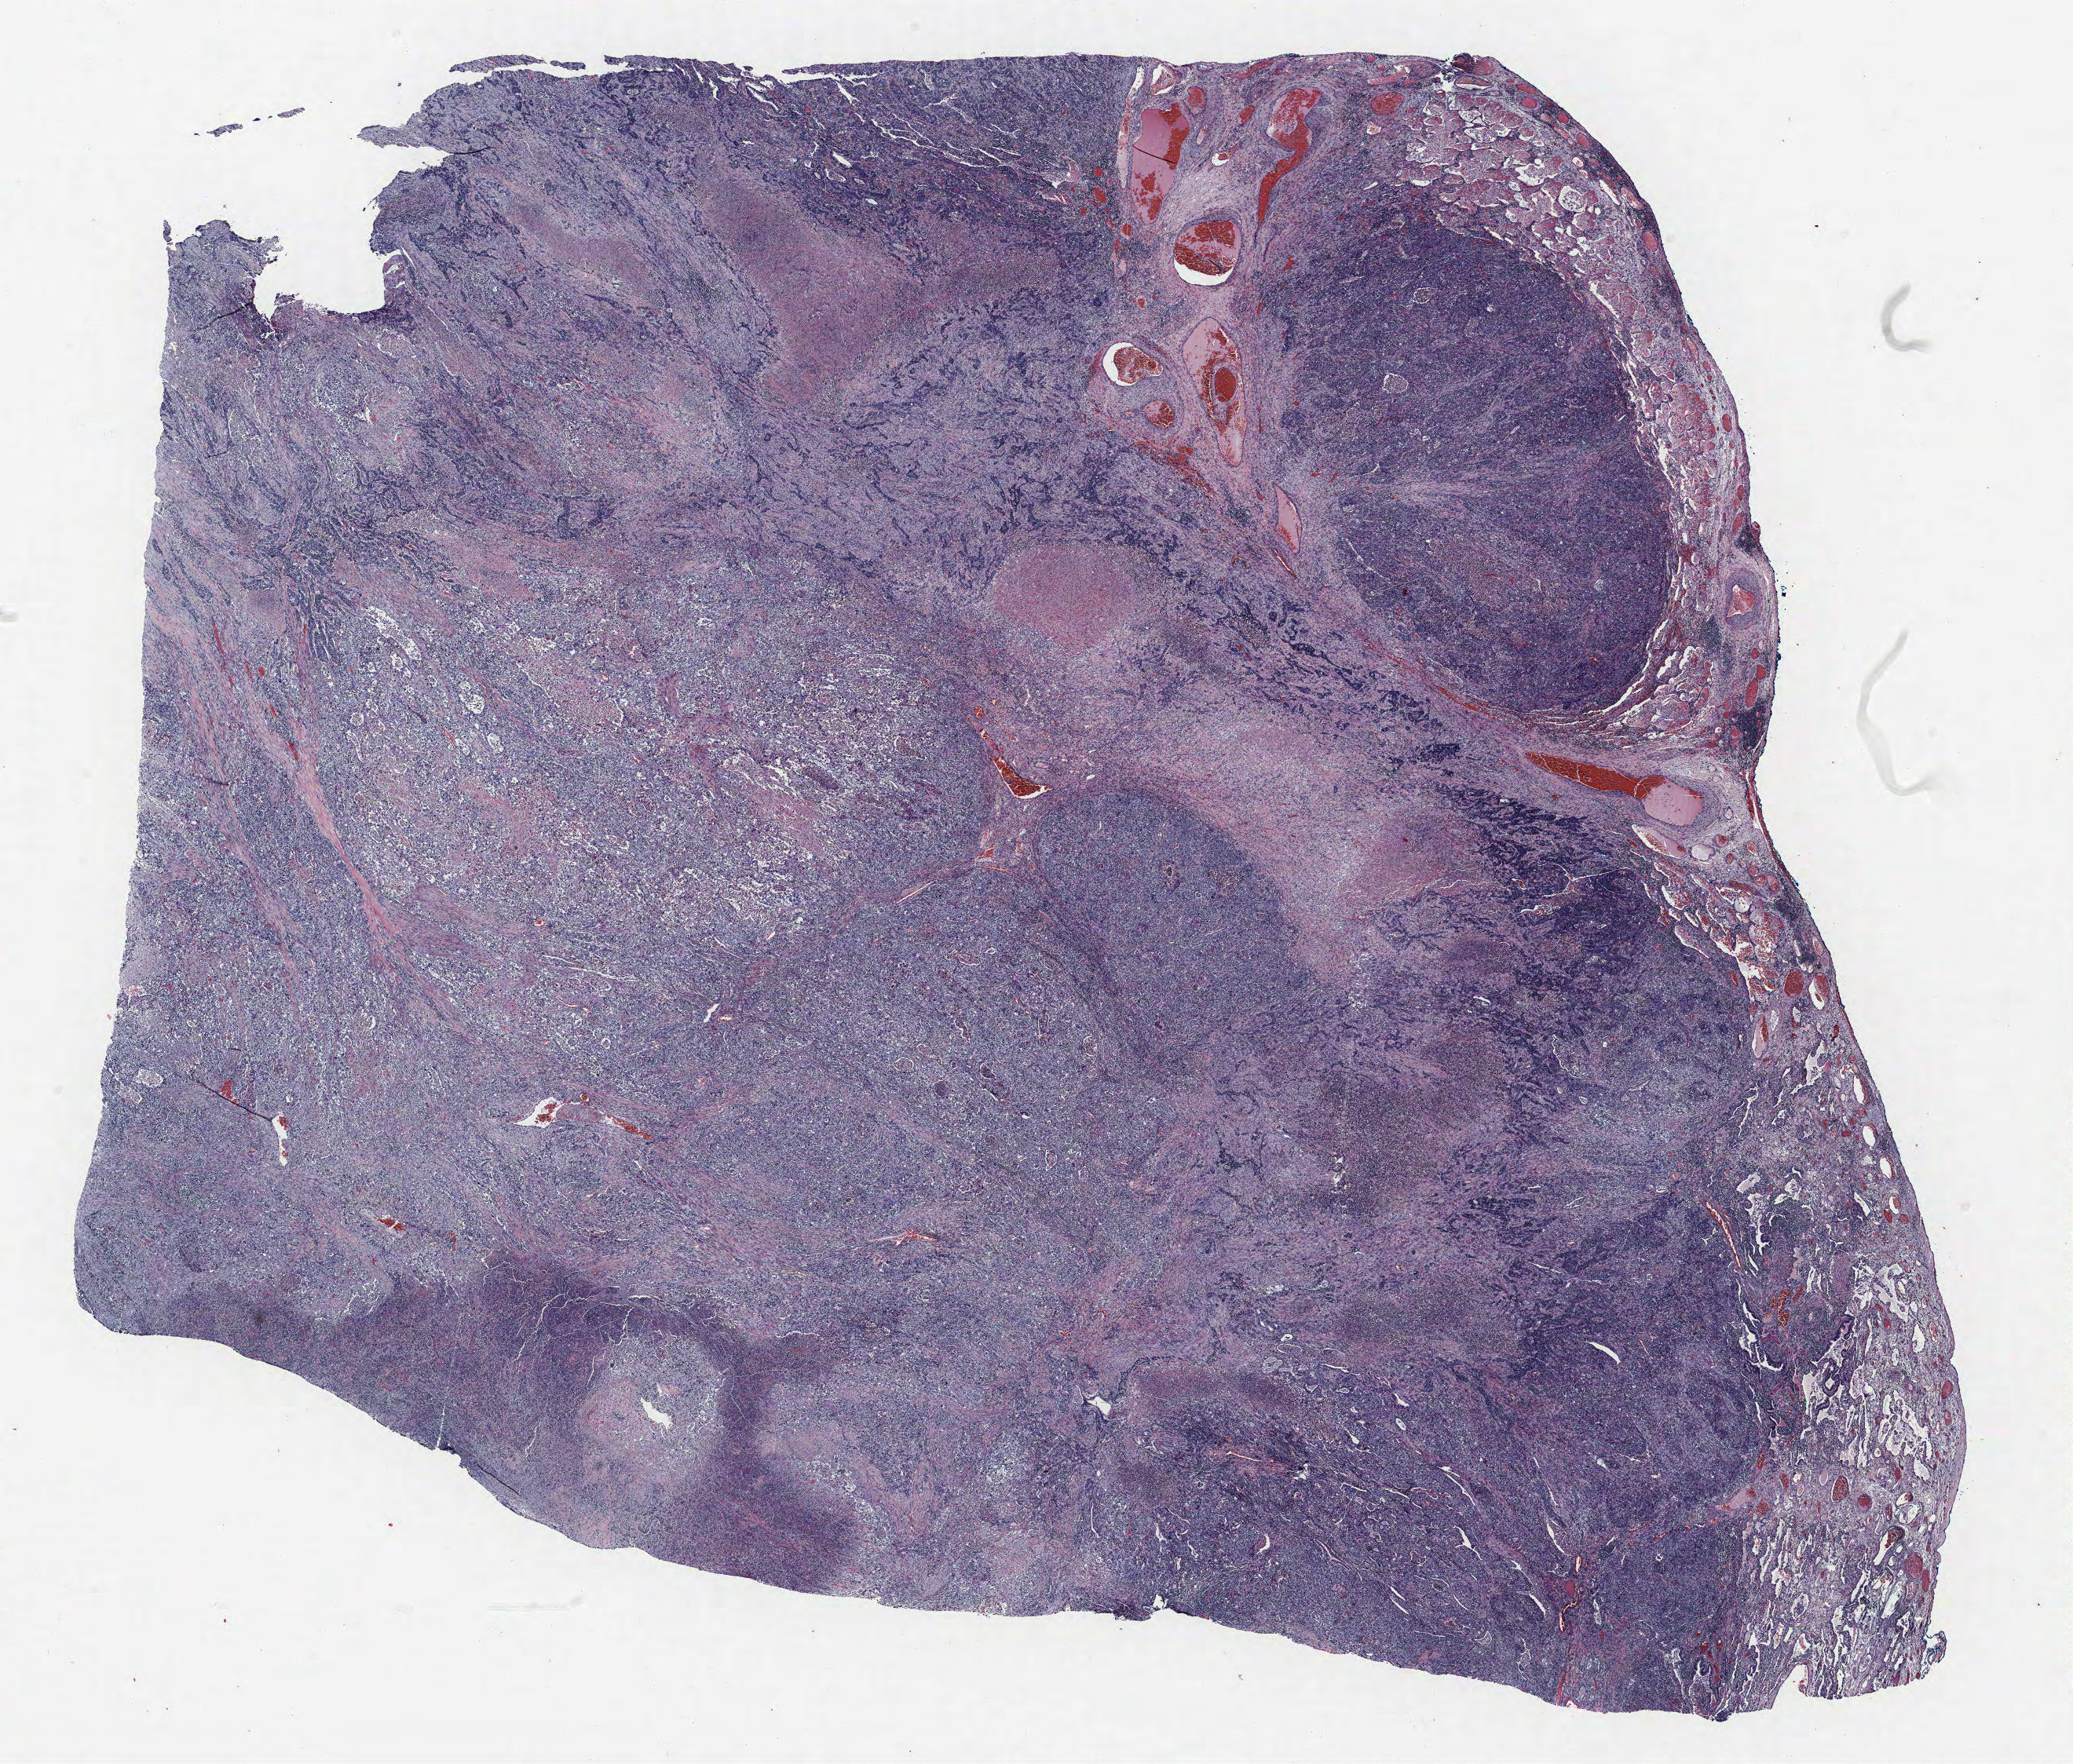
H&E whole-slide image, low-resolution overview of the scanned area, about 21.1 x 18.0 mm. FFPE section. Lung tissue. Female patient, aged 65 at enrolment.
Participant's lung-cancer diagnosis: Squamous cell carcinoma, NOS.